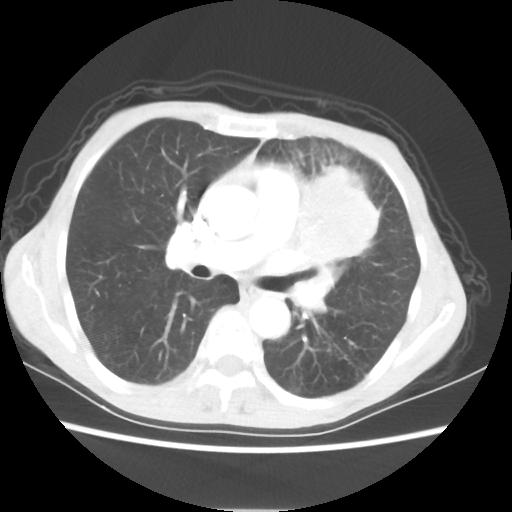
Chest CT, one axial slice. Position 33 of 56 along the scan axis. Reconstruction kernel STANDARD. 80 kVp. Lung window (W 1500 / L -600 HU). 512 × 512 image matrix. Patient: female, 60 years. From the clinical record (not read from this slice): clinical TNM (as recorded): T4 N1 M0.
Outlined on this slice (rectangle marked by the reading radiologist):
- lung tumour (recorded histology: adenocarcinoma): bounding box (x1, y1, x2, y2) in pixels: (301, 154, 399, 279)